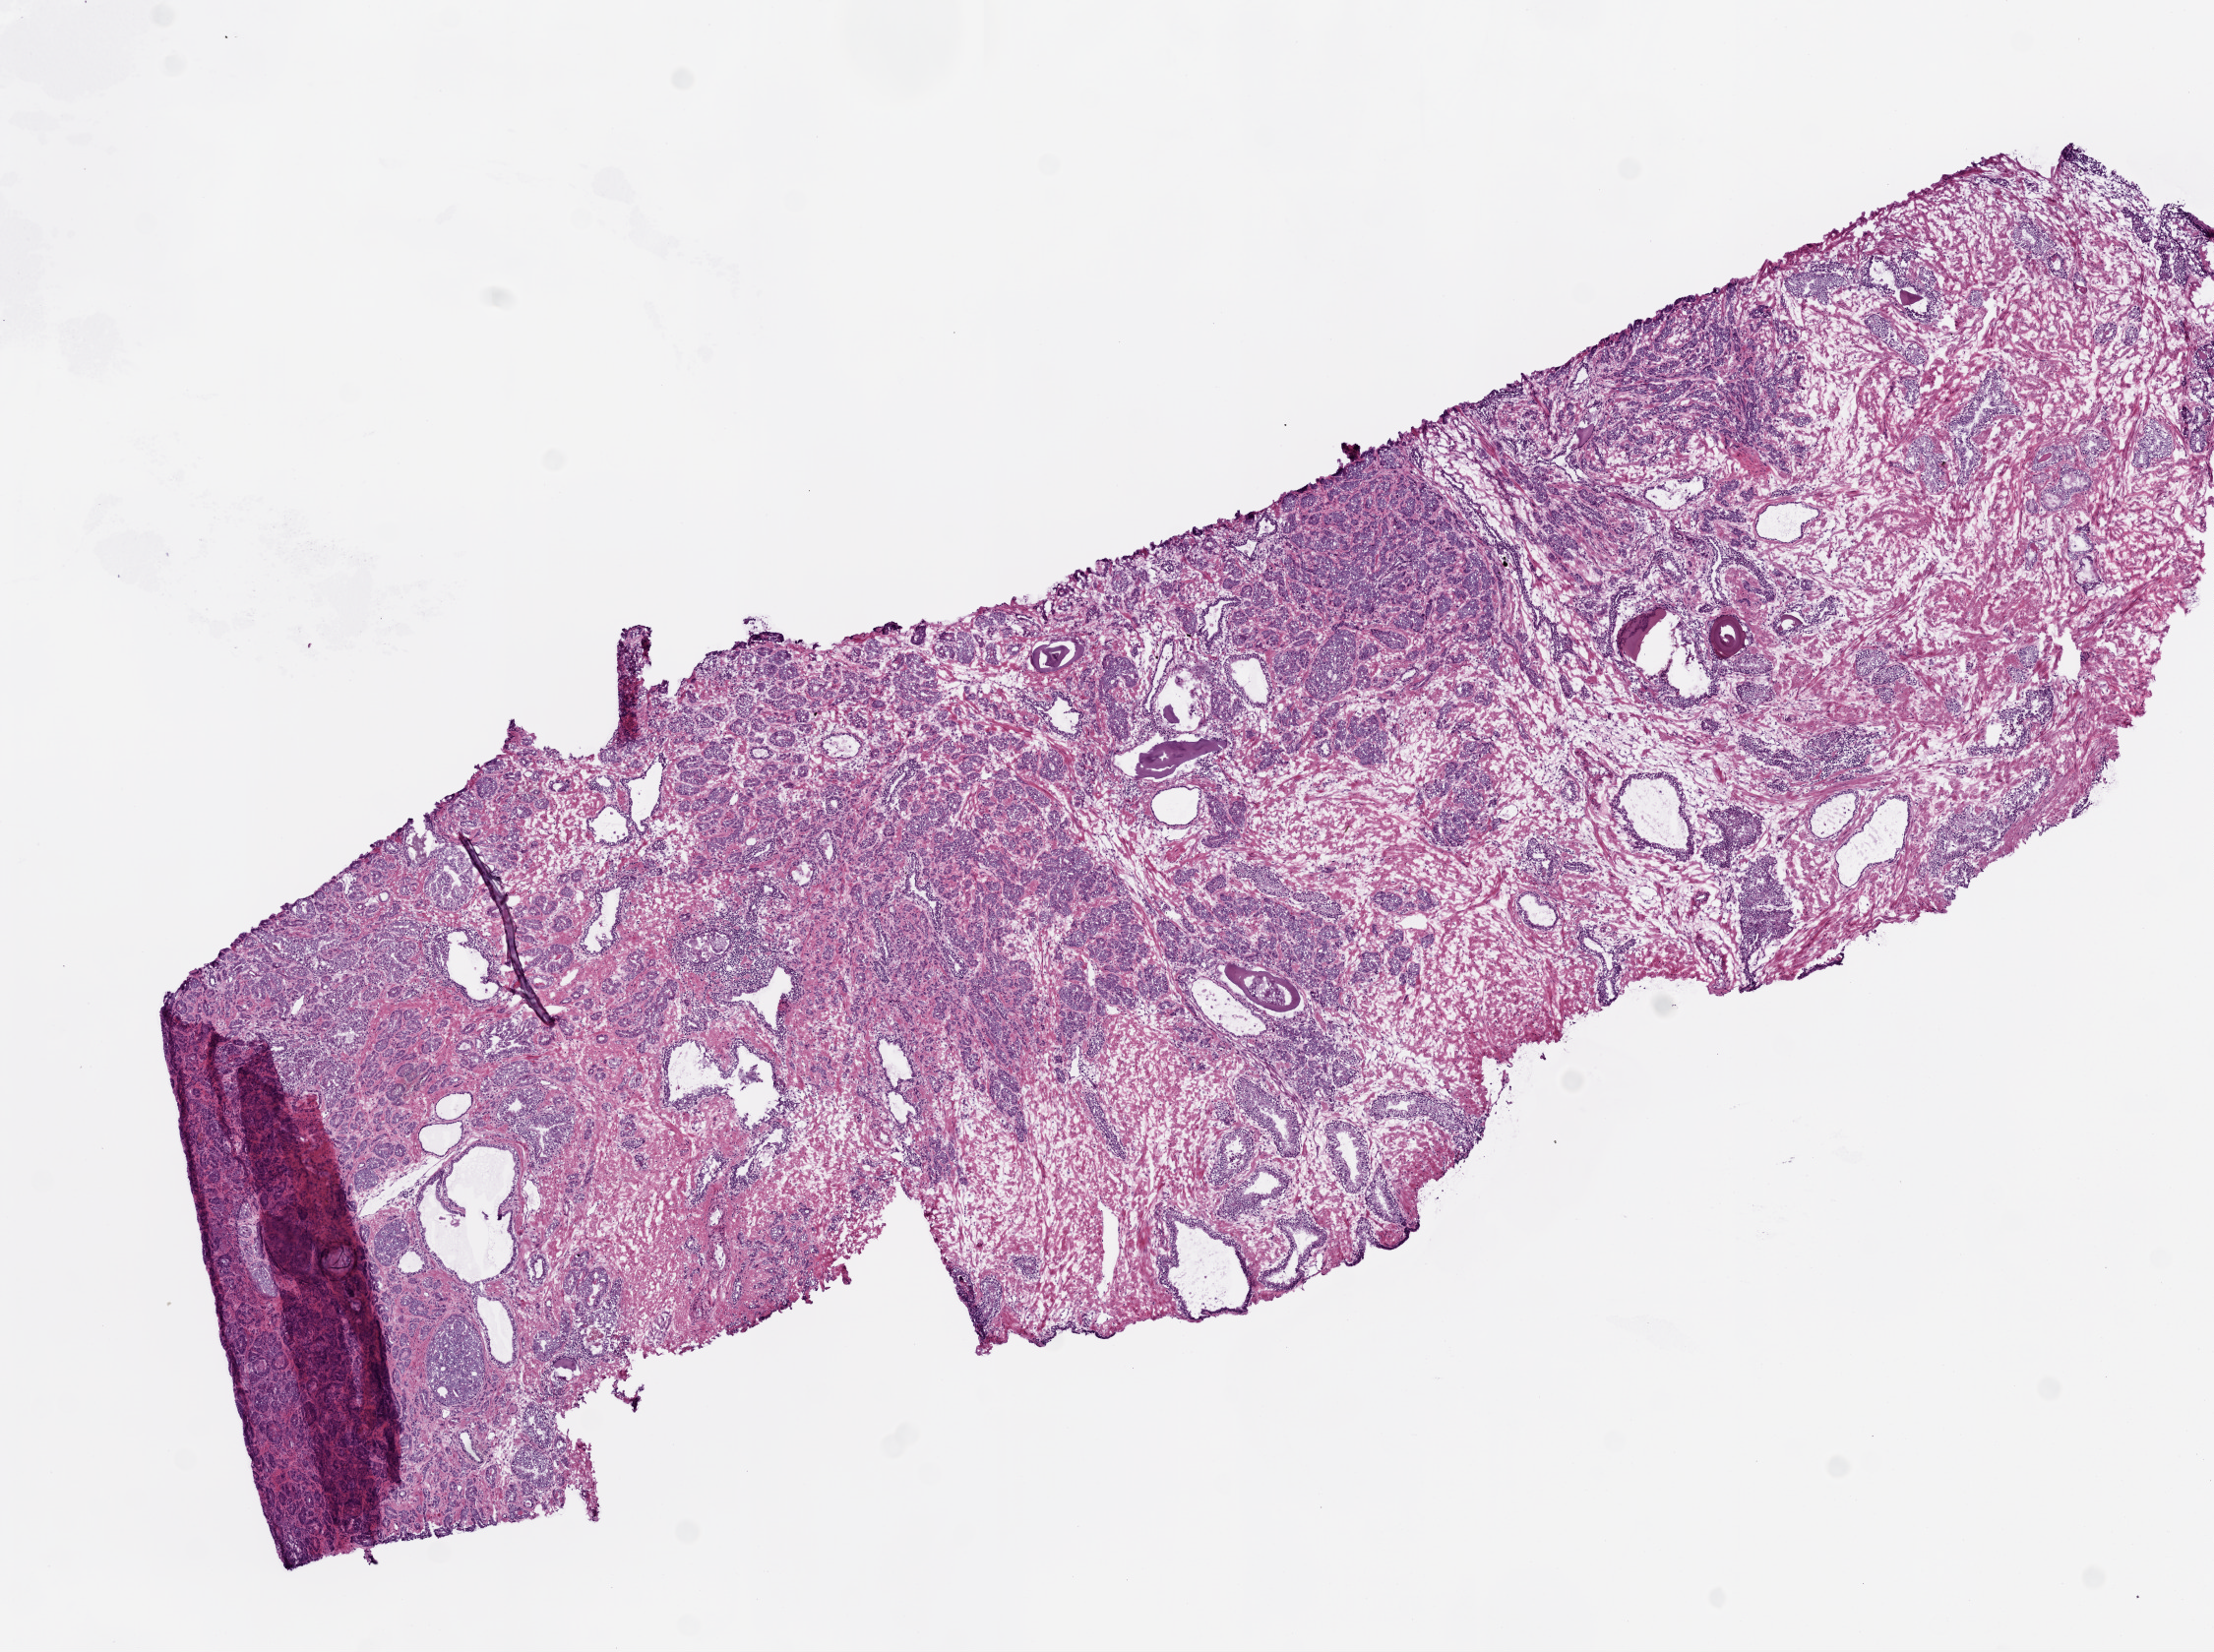
Whole-slide histology image, Hematoxylin and eosin (H&E) stained, whole scanned area (about 9.0 x 6.7 mm, acquisition: 20x scan) shown as a low-resolution overview. Frozen section. Primary tumour sample from the prostate. Male, age 60 years at initial diagnosis. Gleason score: 7 (4+3). Slide review estimates, as recorded: tumour cells 50%, tumour nuclei 60%, normal cells 25%, stromal cells 25%, necrosis 0%. Inflammatory infiltration, as recorded: lymphocyte infiltration 0%, monocyte infiltration 0%, neutrophil infiltration 0%.
• histologic diagnosis: Acinar cell carcinoma (prostate gland)
• lymph nodes positive (case pathology): 0 of 7 examined